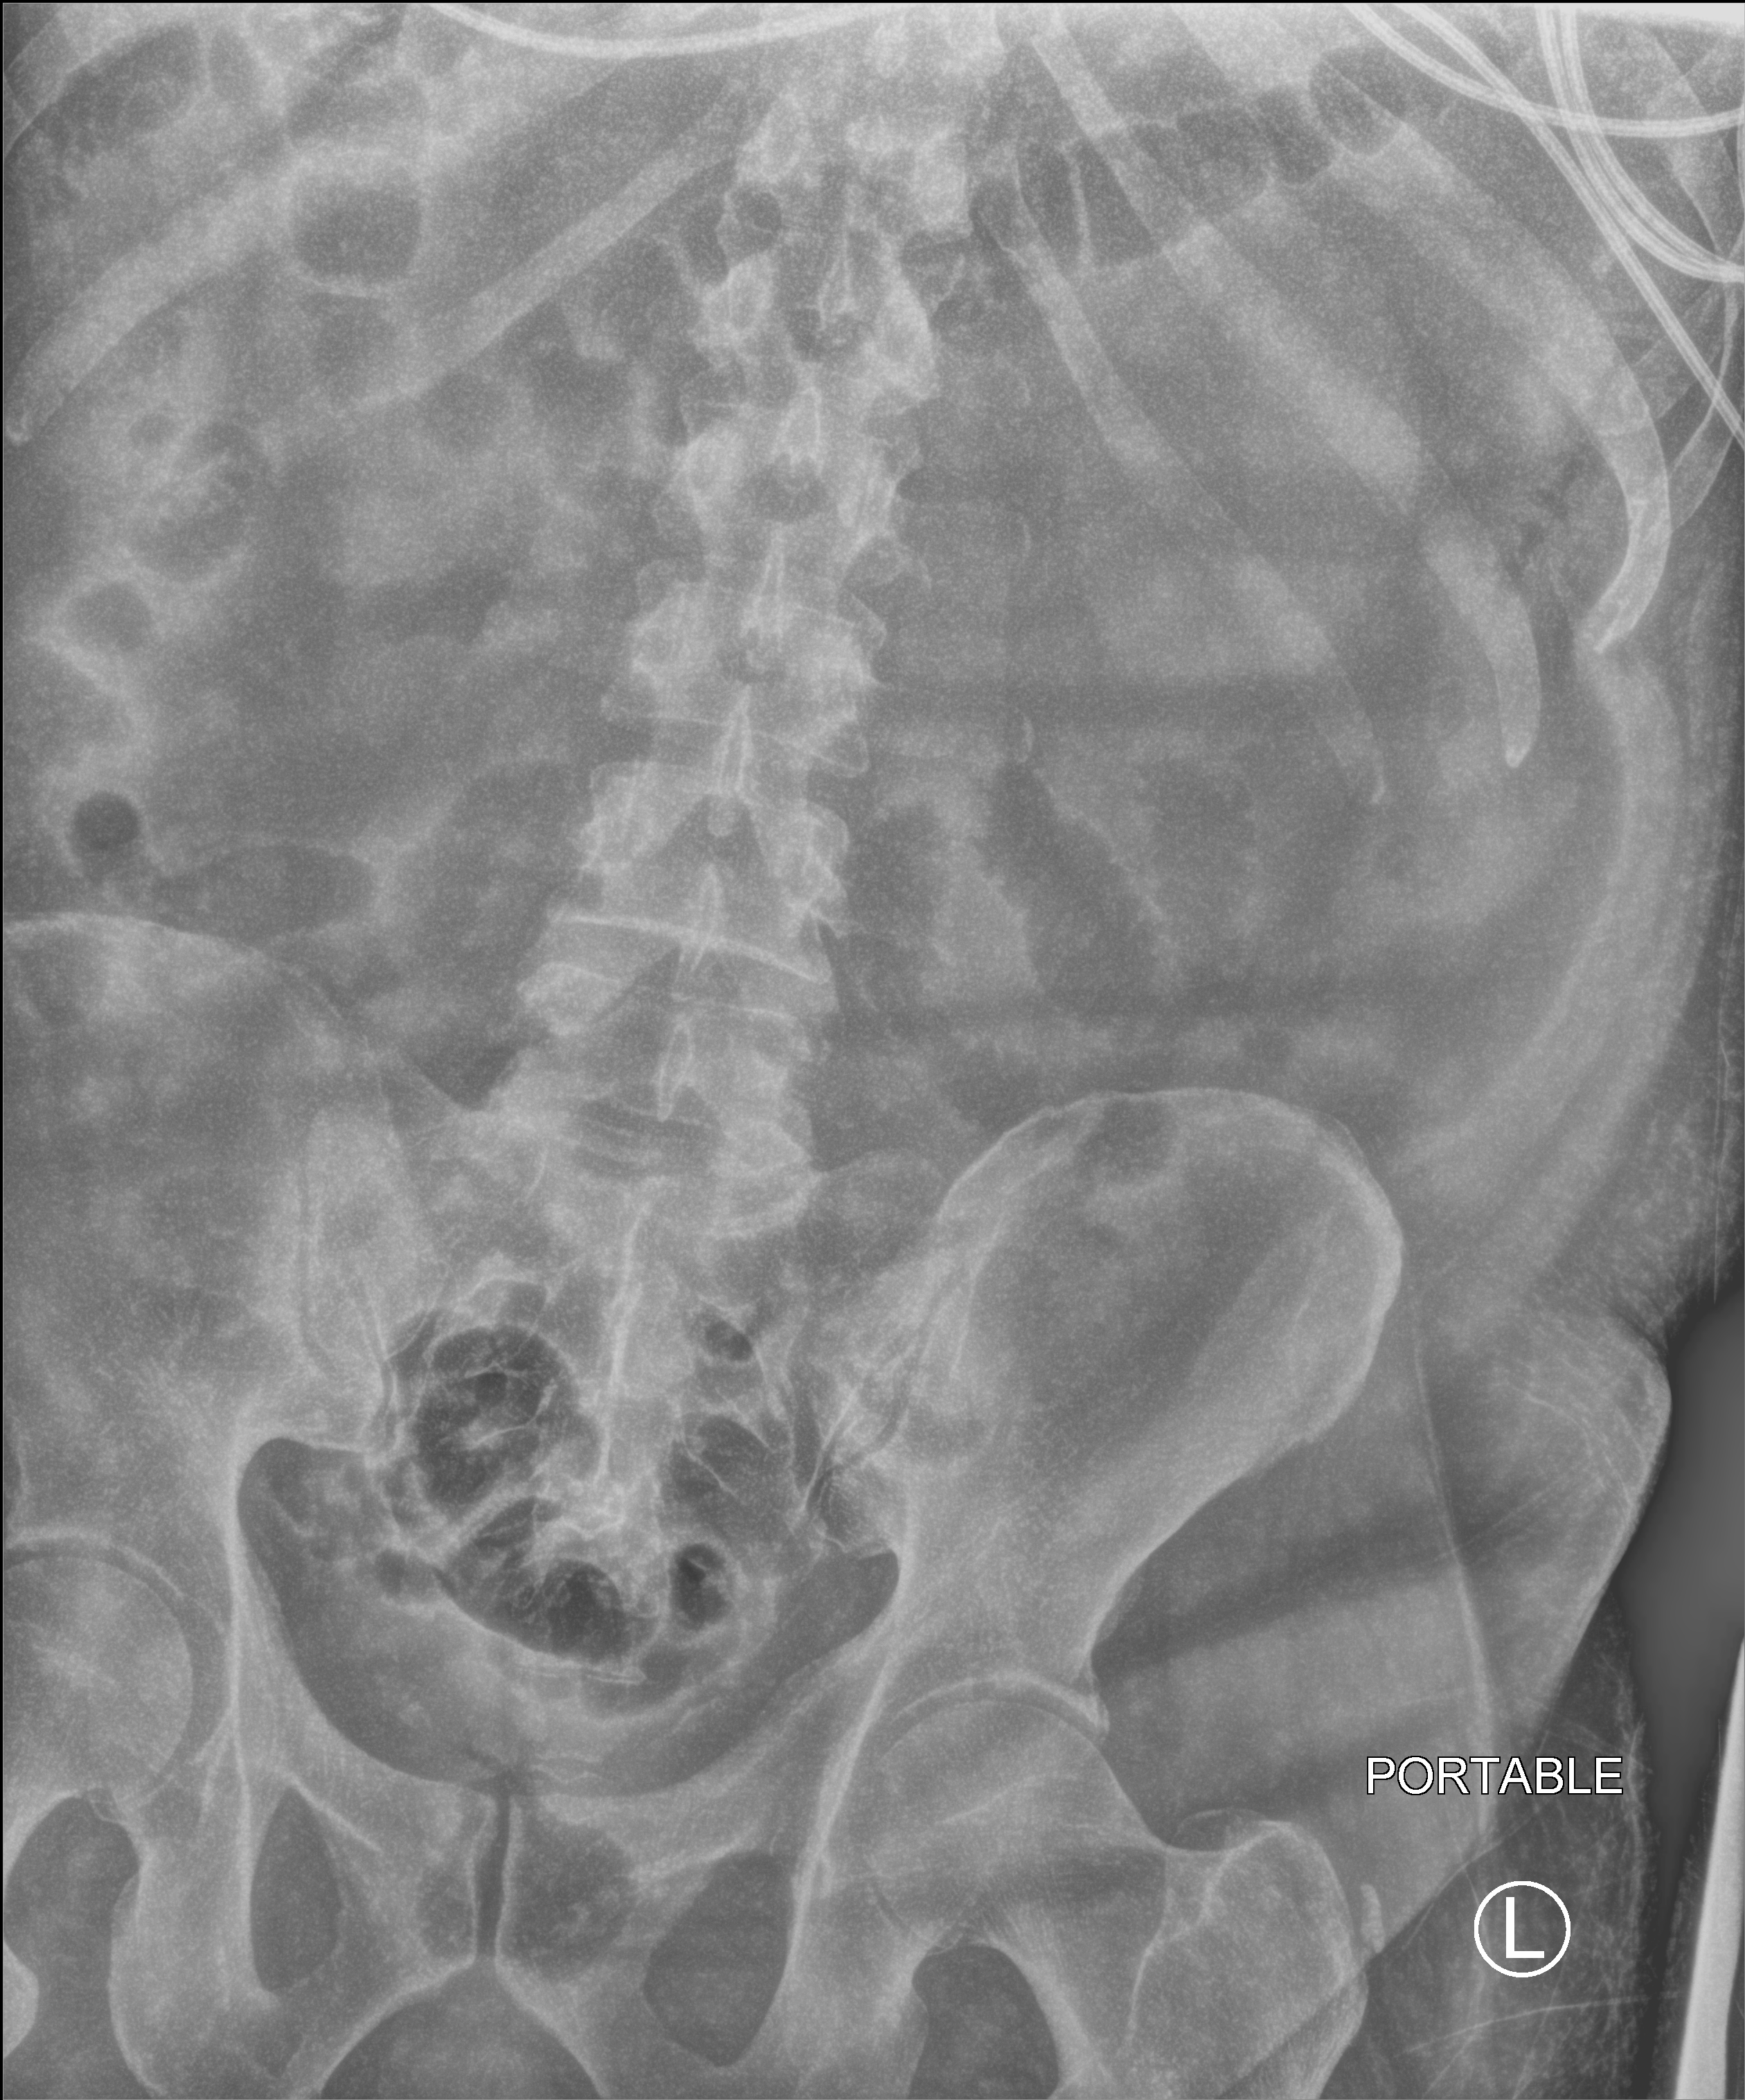
Portable abdomen radiograph; anteroposterior (AP) projection. Patient hospitalised with COVID-19; male, aged 18–59 years.
From the hospital-stay record, not from the radiograph (when in the stay this image was taken is not recorded): other chronic lung disease (admission record): yes; hypertension (admission record): yes; mechanically ventilated during this hospital stay: yes.